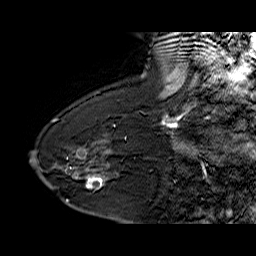
Breast MRI (dynamic contrast-enhanced), one sagittal slice; slice 44 of 60 in the series (ordered by position); dynamic contrast-enhanced series, time point 2 of 6 at this slice position (early post-contrast); 1.5 T; TE 6.4 ms, TR 32.9 ms; 4 mm slice thickness; 256 × 256 image matrix, field of view 200 × 200 mm. Female patient. Case-level facts recorded for this patient, not image findings: setting: breast cancer imaged before/during neoadjuvant chemotherapy; receptor status: HR-positive, HER2-negative.
Structures marked on this image (semi-automatically segmented with operator editing):
- analysis volume of interest (the breast-tissue region the enhancement analysis was run in; not a lesion): bounding box [x1, y1, x2, y2] px = [68, 154, 129, 203]
- tumour enhancement mask (voxels above the 100 % enhancement threshold inside the analysis volume of interest): [76, 176, 107, 189]